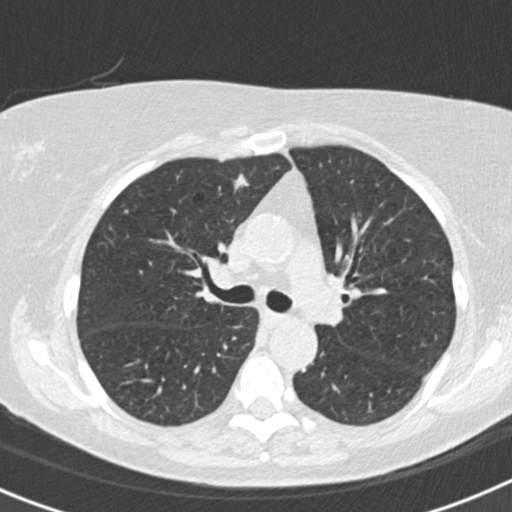
Low-dose screening chest CT, axial slice. Second annual screen. Lung window (W 1500 / L -600 HU). Standard (soft-tissue) reconstruction kernel (B30f). Slice 58 of 160 in the series. Female participant, aged 72 years at enrolment. Former smoker at enrolment.
• Lesion marked by an expert reader, box from (x=213, y=162) to (x=262, y=211) px.
• Screening reader's record for this exam (one nodule recorded; not confirmed to be the boxed lesion): non-calcified nodule or mass ≥4 mm, right upper lobe, 5 × 5 mm, smooth margins, soft tissue attenuation.
• Later outcome: lung cancer diagnosed 462 days after this screen (after the third annual screen) — adenocarcinoma, NOS, right upper lobe, moderately differentiated (G2), stage IA (AJCC 6th edition), 15 mm at pathology.